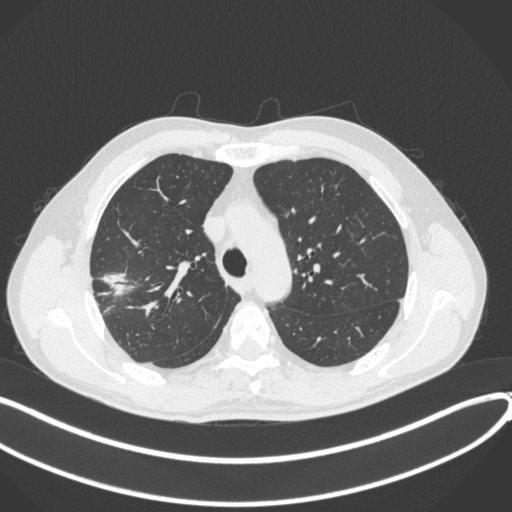
Chest CT, one axial slice; position 306 of 381 along the scan axis; 120 kVp; lung window (W 1500 / L -600 HU); 512 × 512 image matrix, field of view 400 × 400 mm. Patient: male, 62 years. Case-level facts recorded for this patient, not image findings: clinical TNM (as recorded): T1c N0 M0; histopathological grade: G2-3.
Structures marked on this image (bounding box drawn by a radiologist):
- lung tumour (recorded histology: adenocarcinoma): bounding box (x1, y1, x2, y2) in pixels: (99, 264, 135, 293)